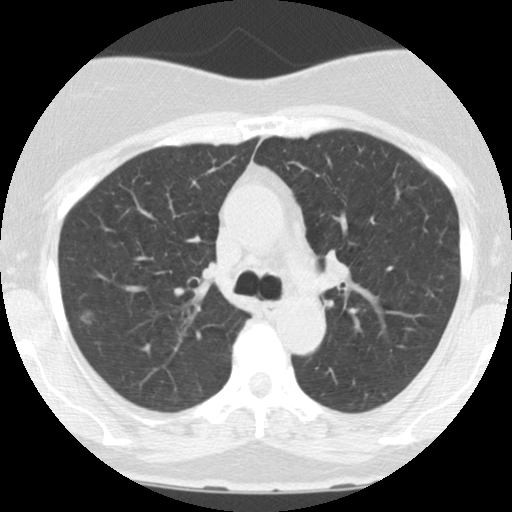
Low-dose screening chest CT, axial slice. Baseline screening round. Lung window (W 1500 / L -600 HU). 2.5 mm slice thickness. 120 kVp. 512 × 512 image matrix, field of view 290 × 290 mm. Female, age 60 years at enrolment. Former smoker at enrolment.
• Expert reader's lesion annotation, bounding box <72,304,103,332> (left, top, right, bottom; pixels).
• The screening reader recorded 3 non-calcified nodules or masses ≥4 mm on this exam (left upper lobe, right upper lobe, right upper lobe); which of them this box marks is not recorded.
• Lung cancer was diagnosed 31 days after this screen: bronchiolo-alveolar adenocarcinoma, NOS, left upper lobe, moderately differentiated (G2), stage IA (AJCC 6th edition), 15 mm at pathology.